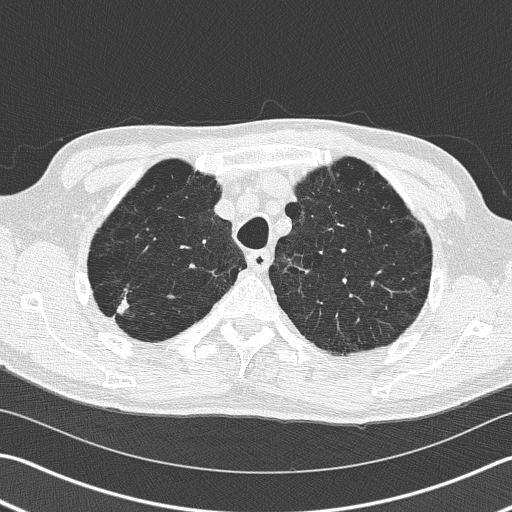
Low-dose screening chest CT, one axial slice. Position 128 of 163 along the scan axis. Reconstruction kernel B50f. 120 kVp. Lung window (W 1500 / L -600 HU). 512 × 512 image matrix, field of view 346 × 346 mm.
Outlined on this slice (manually delineated by an expert):
- lesion 1 (tumor, upper lobe of right lung): bounding box [x1, y1, x2, y2] px = [117, 300, 128, 313]